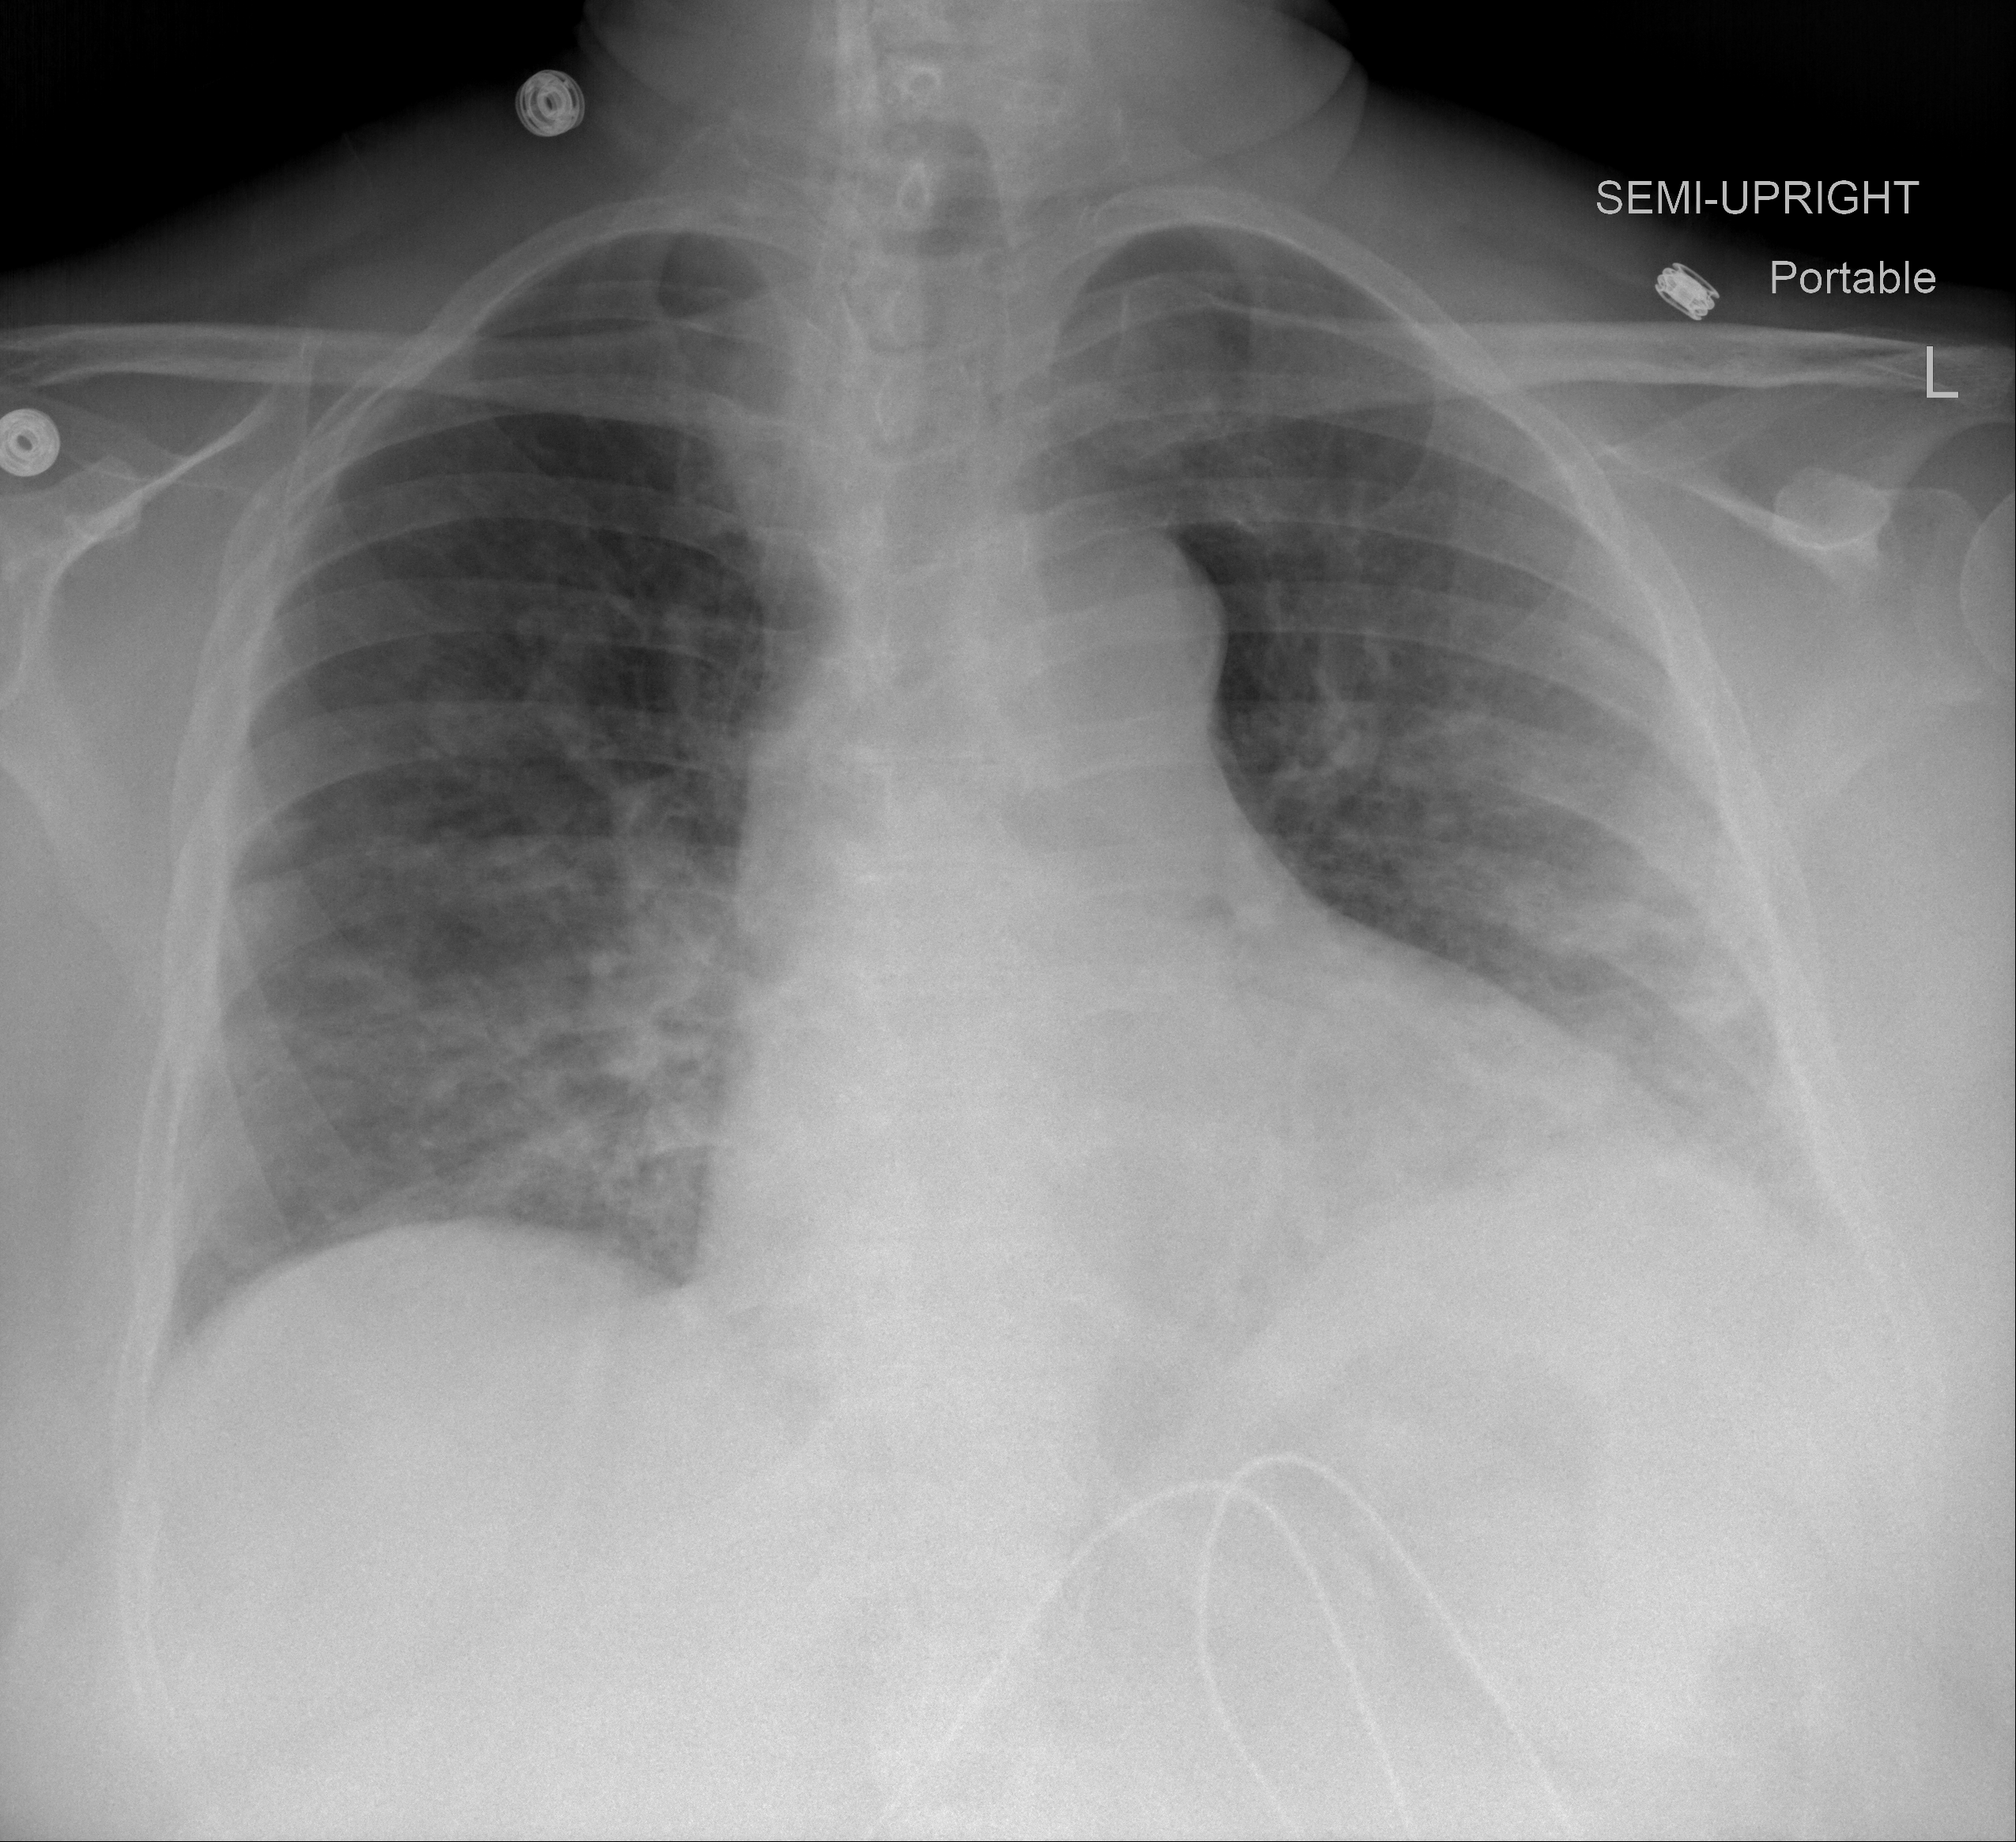
Portable chest radiograph, AP projection. Female patient, age 65 years; imaged 3 days after the COVID-19 diagnosis.
Radiologist key findings (as recorded): patchy and slightly worsened airspace opacities predominately in the lung bases.